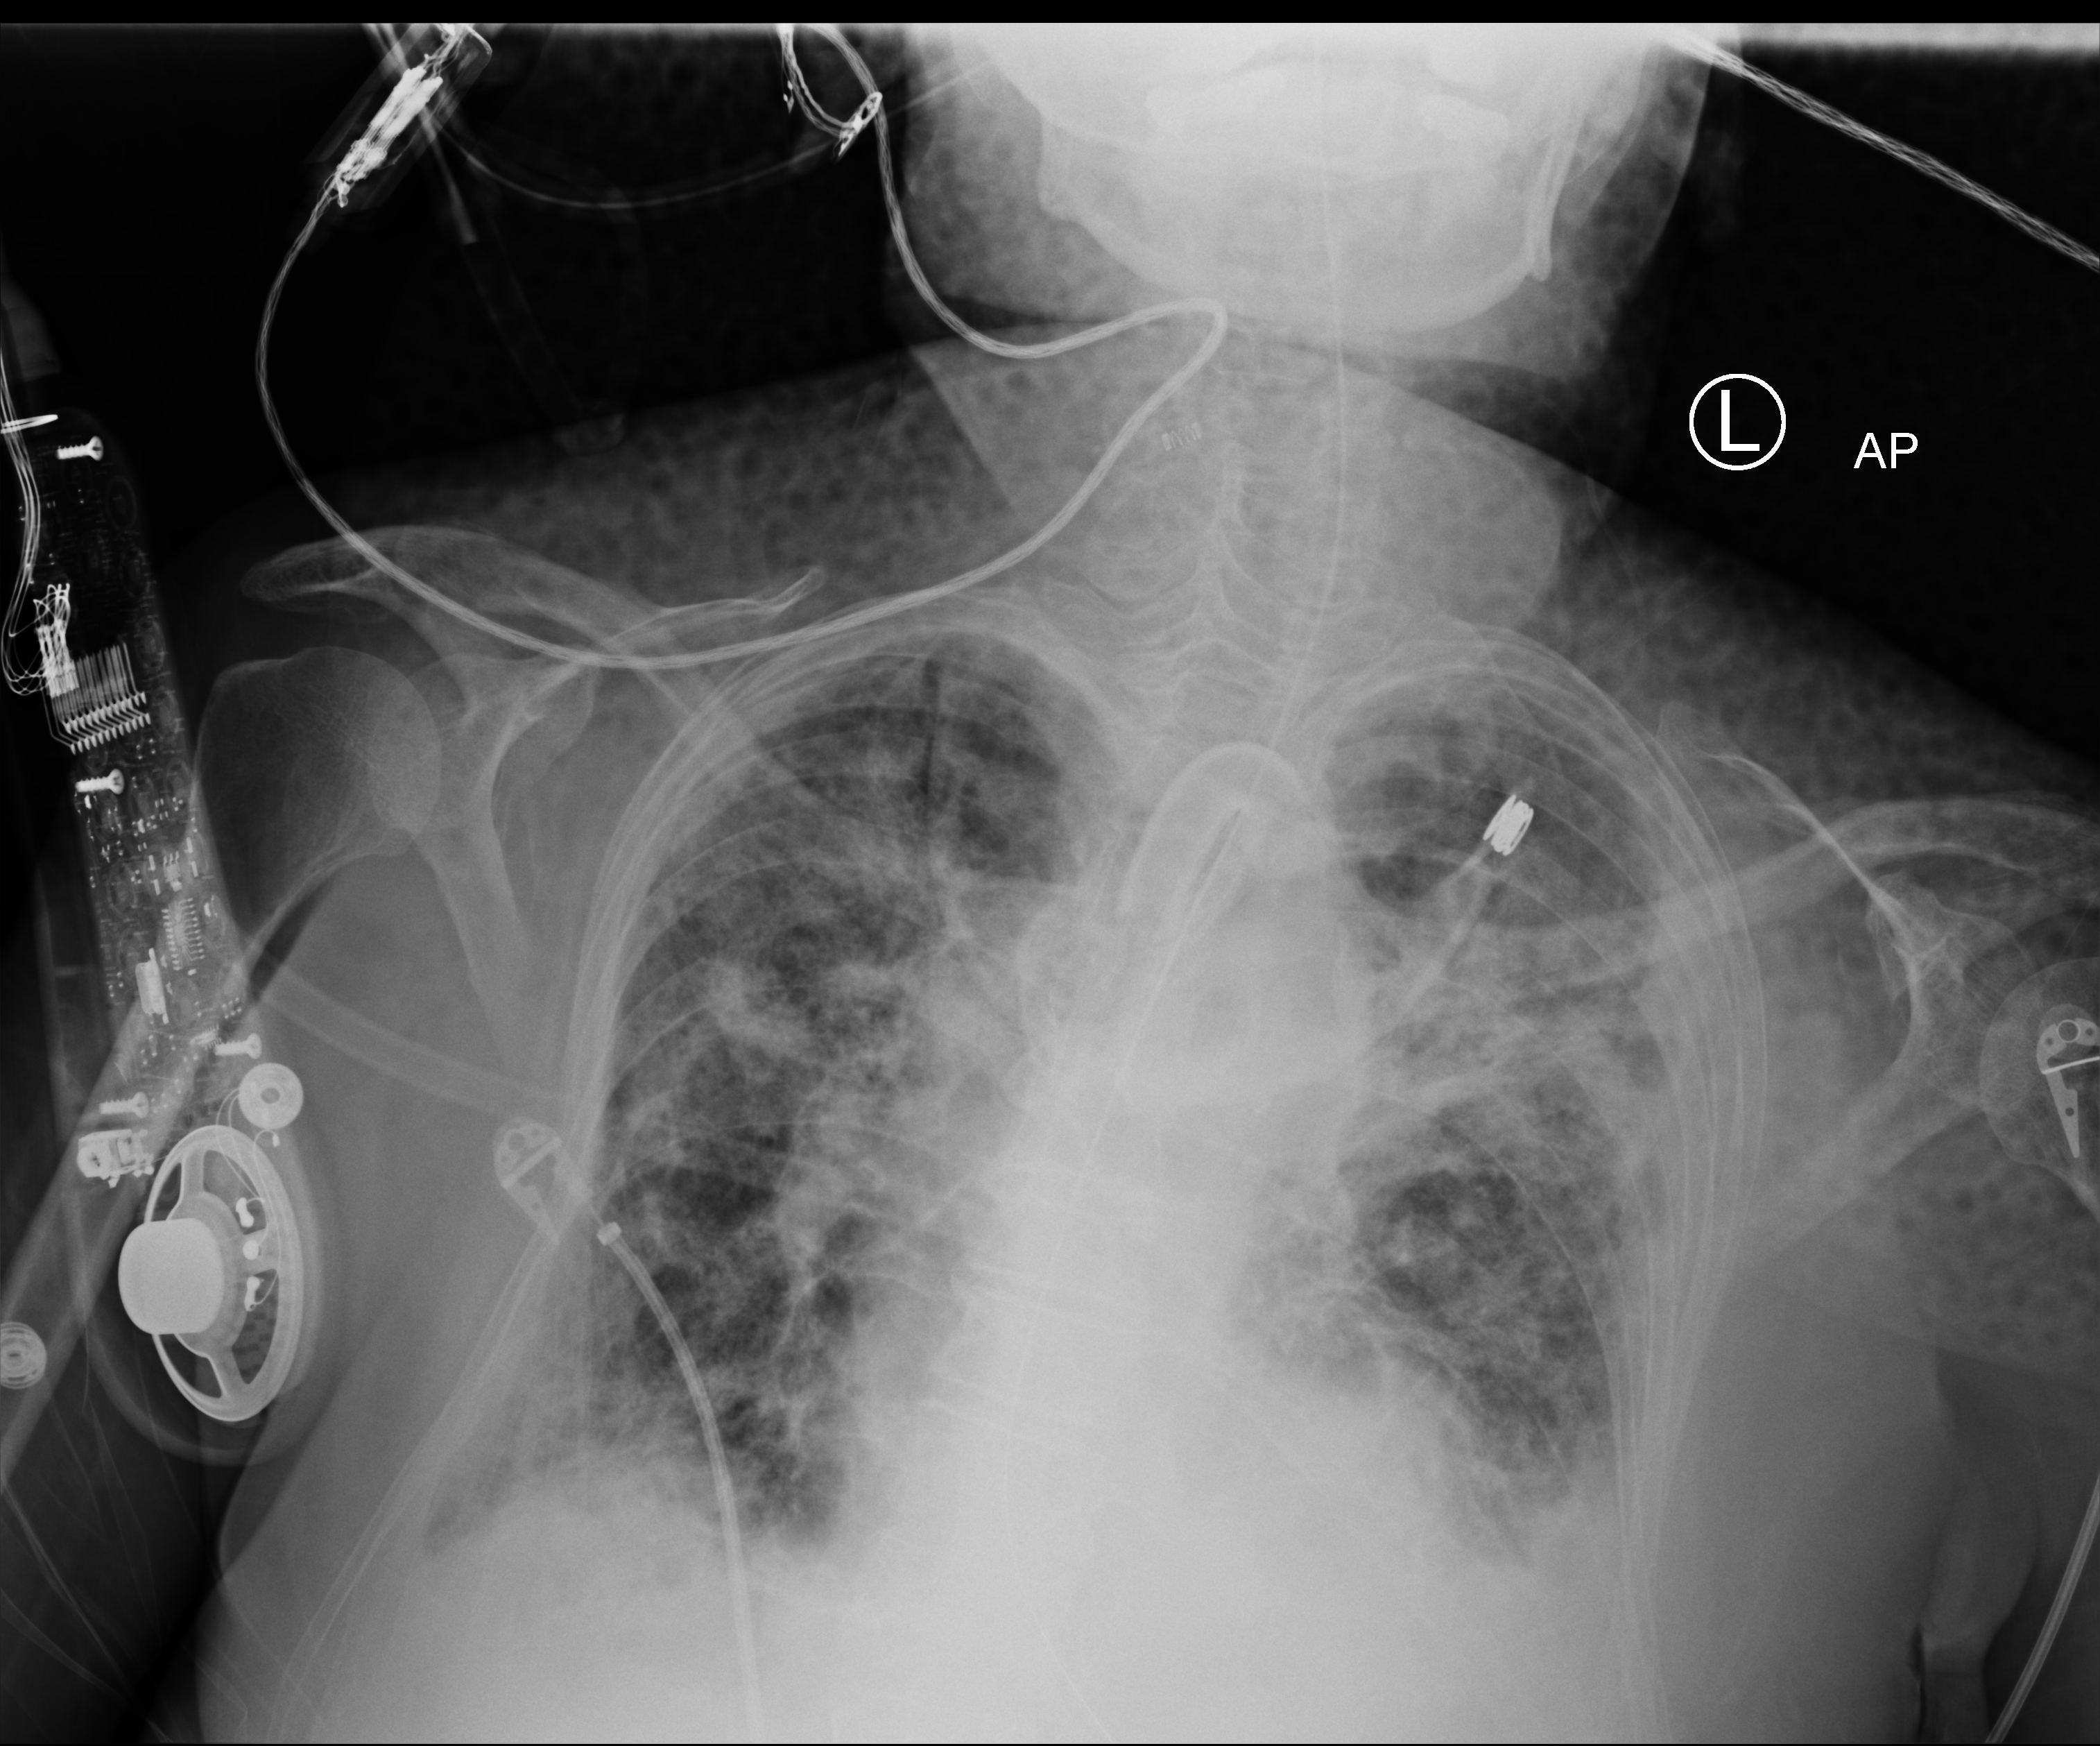
Chest X-ray (portable), anteroposterior (AP) projection. Female patient hospitalised with COVID-19, age 75–90 years.
Admission-level facts for this patient (not findings on this image; timing relative to this image not recorded): admitted to intensive care during this hospital stay: yes.